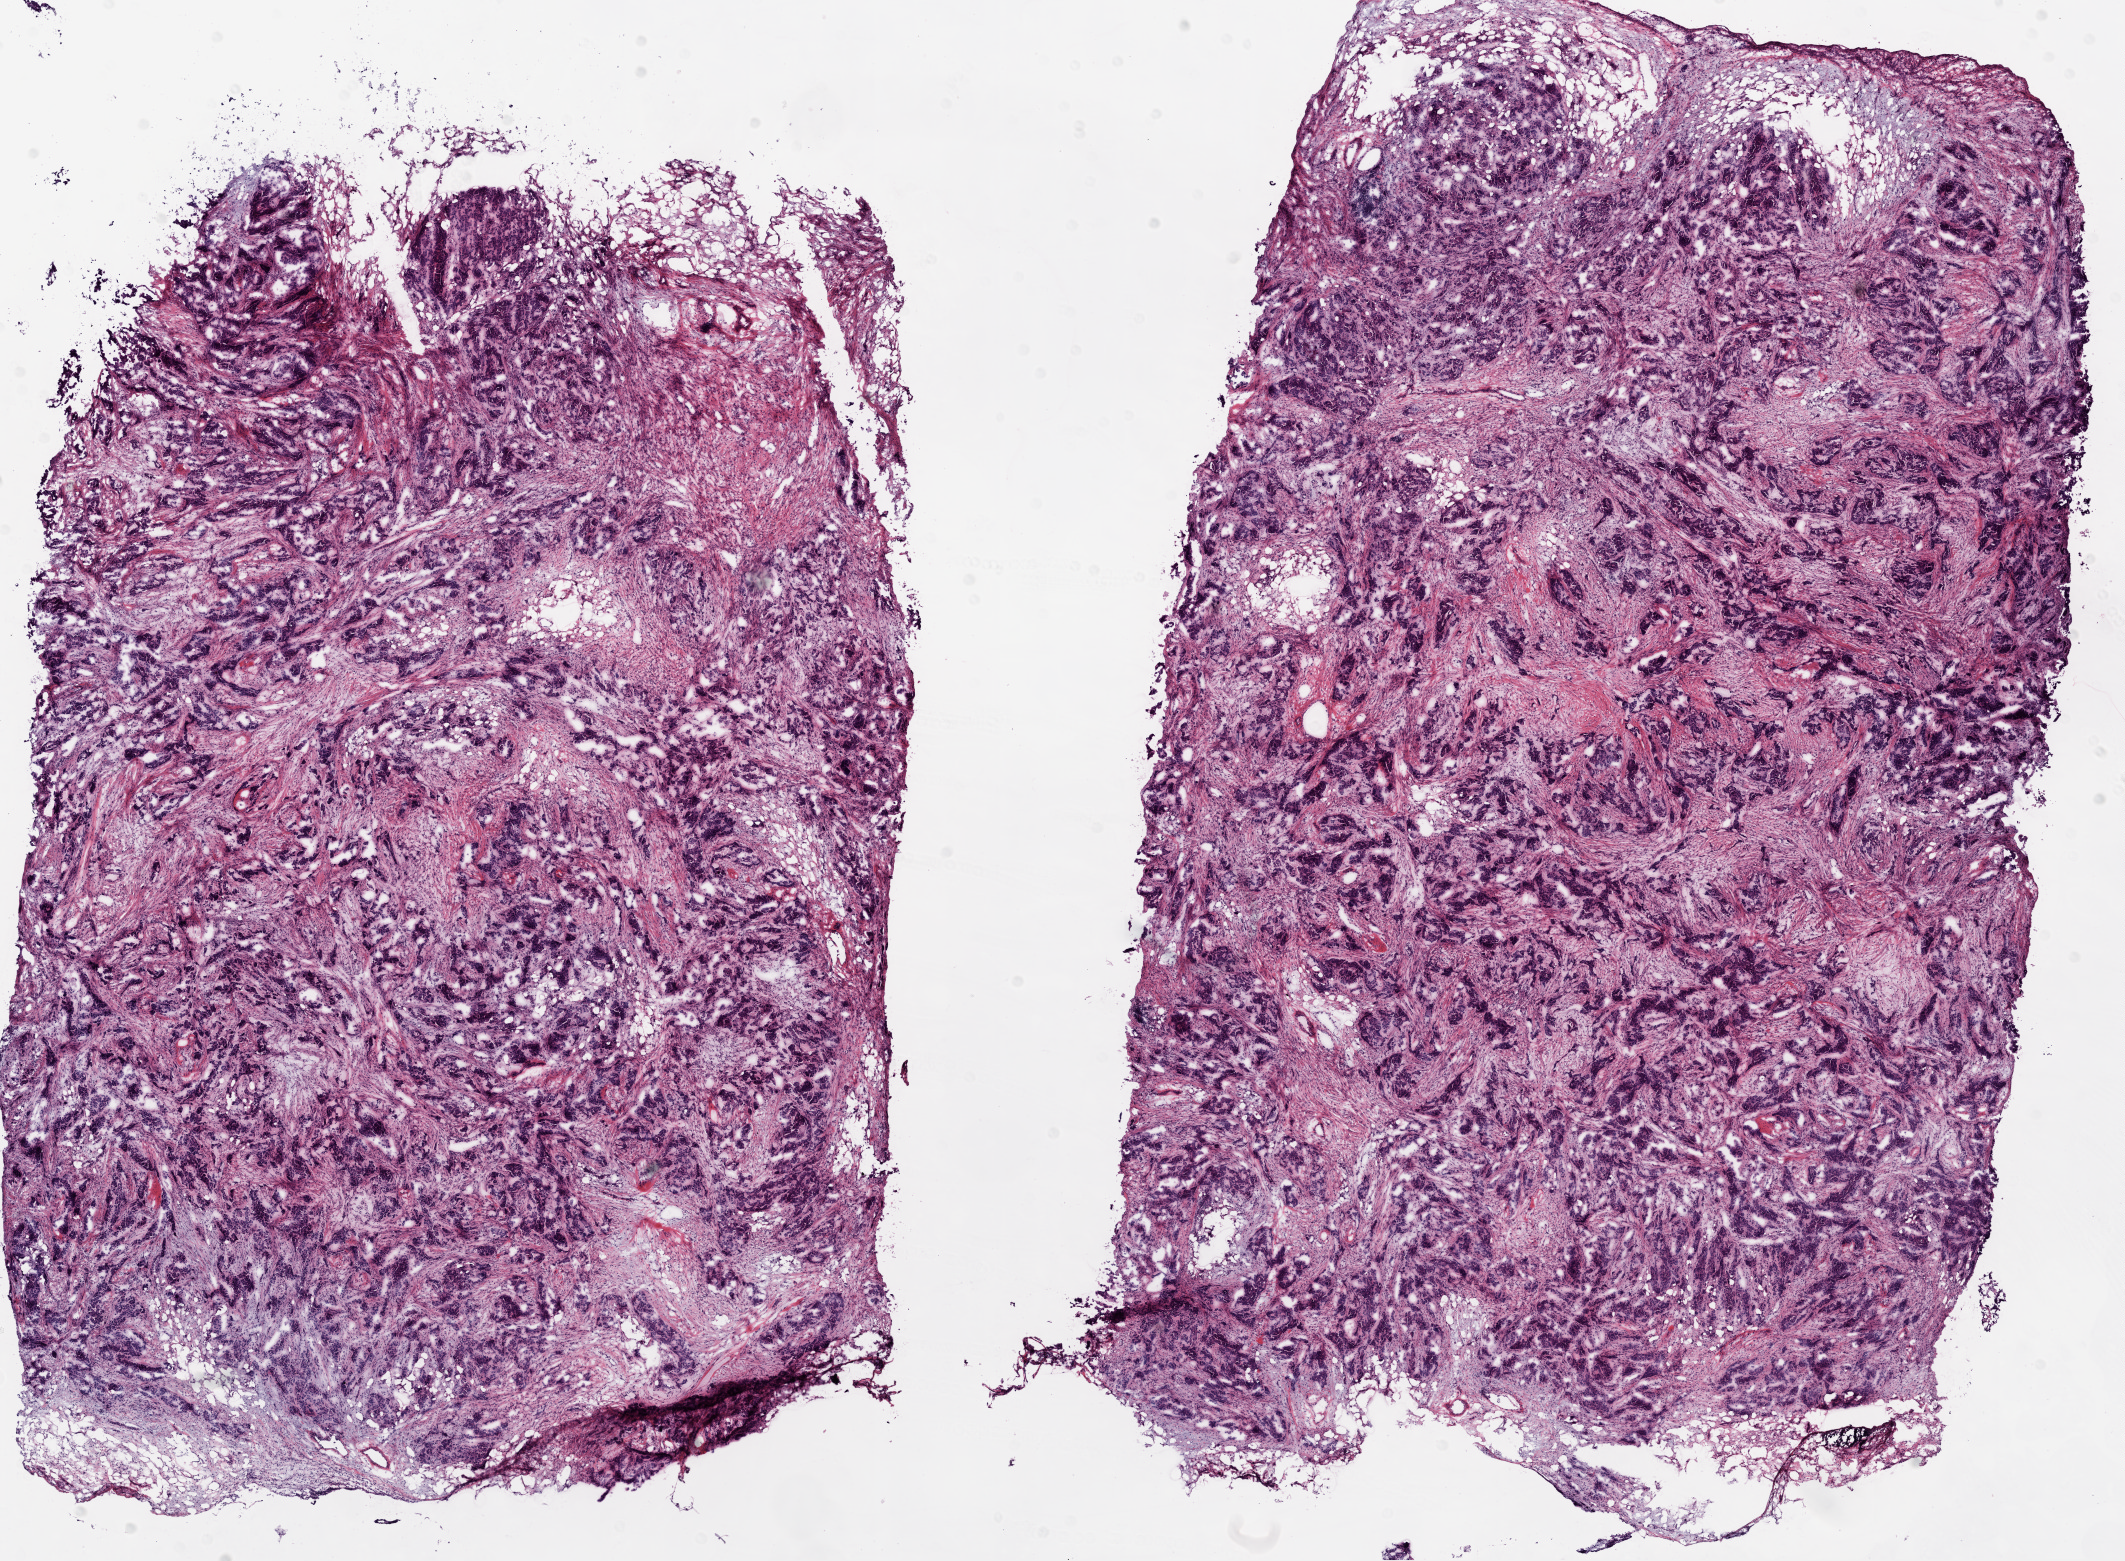
Hematoxylin and eosin (H&E) stained whole-slide image, whole scanned area (about 17.1 x 12.5 mm) shown as a low-resolution overview; frozen section; primary tumour sample from the ovary. Female, age 50 years at initial diagnosis. Histologic grade: G3 (poorly differentiated). Pathologist review of this section (percent, as recorded): tumour cells 70%, tumour nuclei 70%, normal cells 0%, stromal cells 30%, necrosis 0%.
Laterality: bilateral. Diagnosis: Serous cystadenocarcinoma, NOS. FIGO stage: IV.